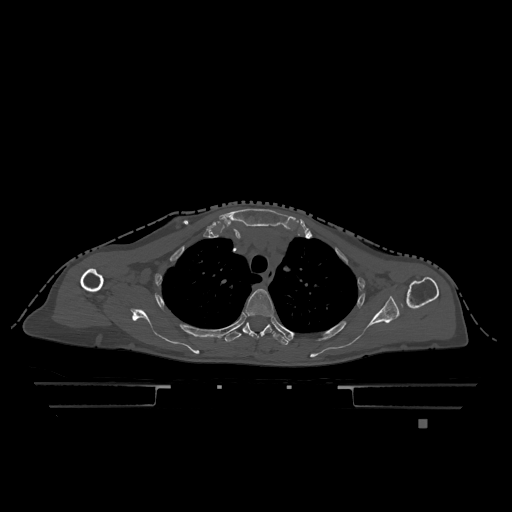
CT including the spine, one axial slice. Bone window (W 1800 / L 400 HU). 0.5 mm slice thickness. 512 × 512 image matrix, field of view 500 × 500 mm. Female patient, age 74 years. From the clinical record (not read from this slice): primary cancer: lung.
Annotated regions visible in this slice (semi-automatic segmentation, software-assisted and operator-edited):
- T3 vertebra: bounding box <245,289,274,317> (left, top, right, bottom; pixels)
- T4 vertebra: <224,322,293,345>